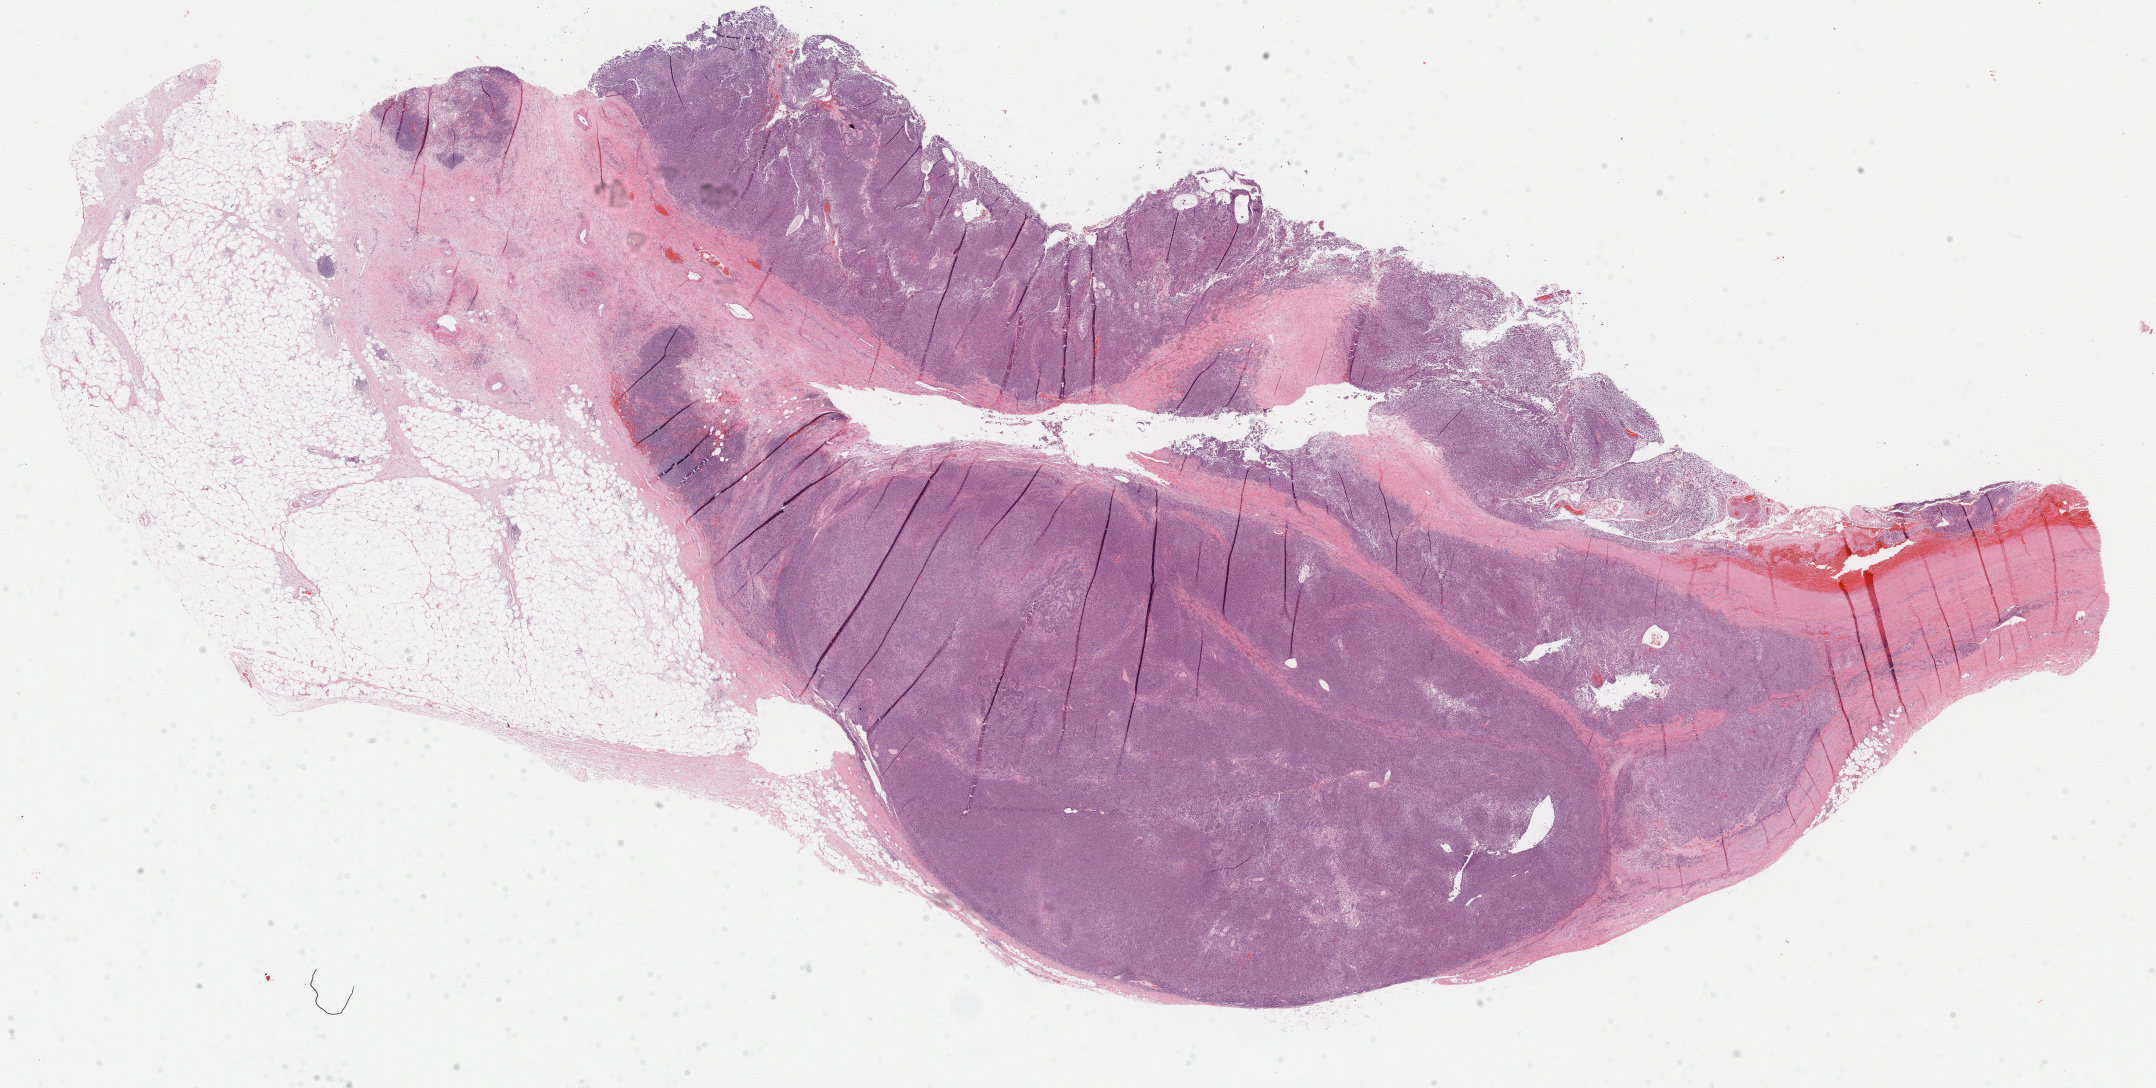
Digitized Hematoxylin and eosin (H&E) stained tissue section (whole slide), a low-resolution overview of the entire scanned area, about 34.0 x 17.2 mm, formalin-fixed paraffin-embedded (FFPE) diagnostic section, metastatic tumour sample. Patient: male, age at initial diagnosis 71 years.
- this section: metastatic tumour tissue
- patient diagnosis: Malignant melanoma, NOS